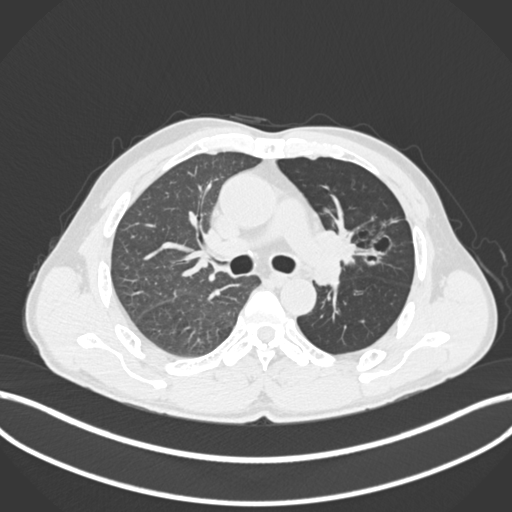
Chest CT, one axial slice; position 119 of 255 along the scan axis; reconstruction kernel B30f; lung window (W 1500 / L -600 HU); 1 mm slice thickness; 512 × 512 image matrix, field of view 400 × 400 mm. Patient: male, 57 years. From the clinical record (not read from this slice): clinical TNM (as recorded): T2b N0 M0.
Structures marked on this image (rectangle marked by the reading radiologist):
- lung tumour (recorded histology: squamous cell carcinoma): box from (x=318, y=224) to (x=367, y=269) px